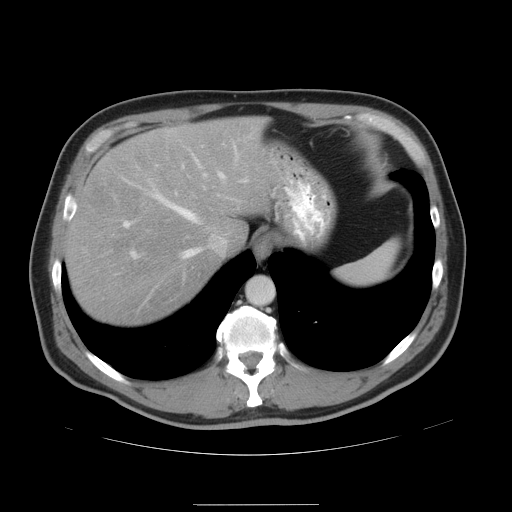
Contrast-enhanced abdominal CT, one axial slice; position 38 of 47 along the scan axis; intravenous contrast given; soft-tissue window (W 400 / L 40 HU); 5 mm slice thickness; 512 × 512 image matrix, field of view 420 × 420 mm. Male patient, age 61 years. Case-level facts recorded for this patient, not image findings: diagnosis: colorectal cancer liver metastases, imaged before liver resection; multiple liver metastases: no; largest metastasis: 1.2 cm; disease in both lobes: no.
Outlined on this slice (manually delineated by an expert):
- hepatic veins: bounding box <136,146,237,258> (left, top, right, bottom; pixels)
- liver: <66,117,279,326>
- planned liver remnant (the part of the liver to remain after resection): <66,117,279,326>
- portal vein (with intrahepatic branches): <124,166,249,257>